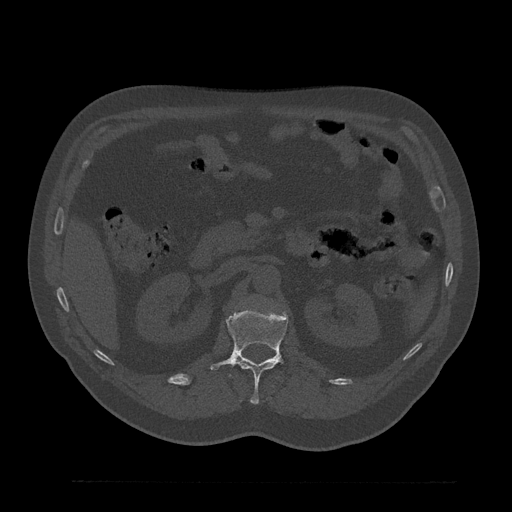
CT including the spine, one axial slice. Position 159 of 797 along the scan axis. Reconstruction kernel Br40s/3. 120 kVp. Bone window (W 1800 / L 400 HU). 0.5 mm slice thickness. 512 × 512 image matrix, field of view 430 × 430 mm. Patient: male, 61 years. From the clinical record (not read from this slice): primary cancer: prostate.
Structures marked on this image (semi-automatically segmented with operator editing):
- L1 vertebra: bounding box (x1, y1, x2, y2) in pixels: (210, 308, 288, 405)